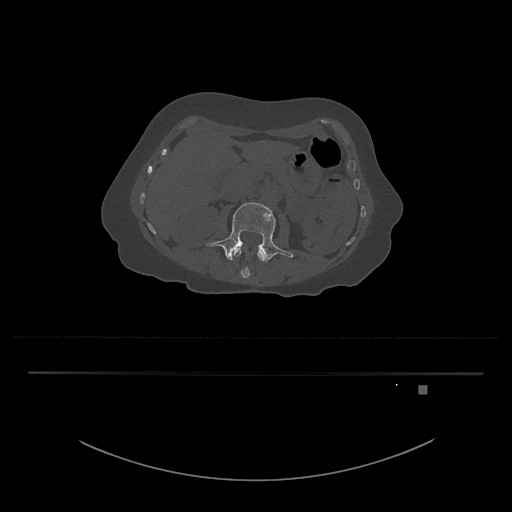
CT including the spine, one axial slice; position 444 of 797 along the scan axis; 120 kVp; bone window (W 1800 / L 400 HU); 0.5 mm slice thickness; 512 × 512 image matrix, field of view 500 × 500 mm. Patient: female, 57 years. Case-level facts recorded for this patient, not image findings: primary cancer: cervical.
Annotated regions visible in this slice (semi-automatic segmentation, software-assisted and operator-edited):
- L3 vertebra: bounding box [x1, y1, x2, y2] px = [206, 202, 294, 263]